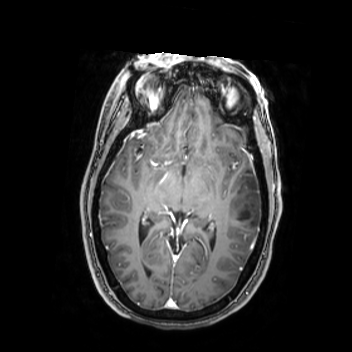
Brain MRI from a brain-tumour surgery series, one axial slice. Slice 149 of 350 in the series (ordered by position). T1-weighted post-contrast. 0.9 mm slice thickness. 352 × 352 image matrix, field of view 280 × 280 mm. Case-level facts recorded for this patient, not image findings: histopathology: Oligodendroglioma; WHO grade: 2; IDH mutation: yes; tumour location: Left Middle Temporal Gyrus.
Structures marked on this image (manually delineated by an expert):
- tumour: box from (x=224, y=174) to (x=262, y=232) px